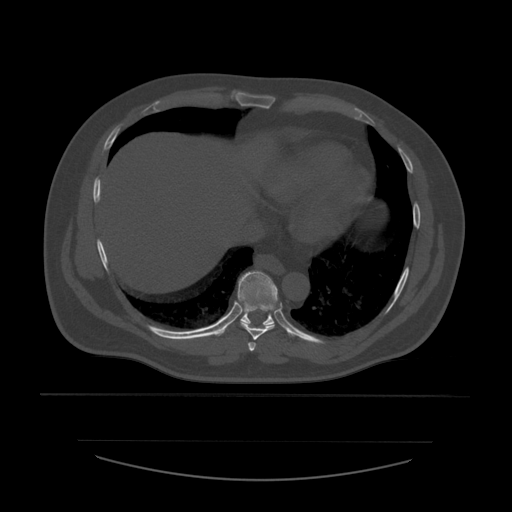
CT including the spine, one axial slice; slice 329 of 532 in the series (ordered by position); reconstruction kernel STANDARD; bone window (W 1800 / L 400 HU); 512 × 512 image matrix, field of view 441 × 441 mm. Patient age 44 years. From the clinical record (not read from this slice): primary cancer: soft tissue sarcoma.
Annotated regions visible in this slice (semi-automatically segmented with operator editing):
- T7 vertebra: bounding box [x1, y1, x2, y2] px = [248, 342, 256, 353]
- T8 vertebra: [241, 322, 276, 341]
- T9 vertebra: [217, 271, 290, 336]